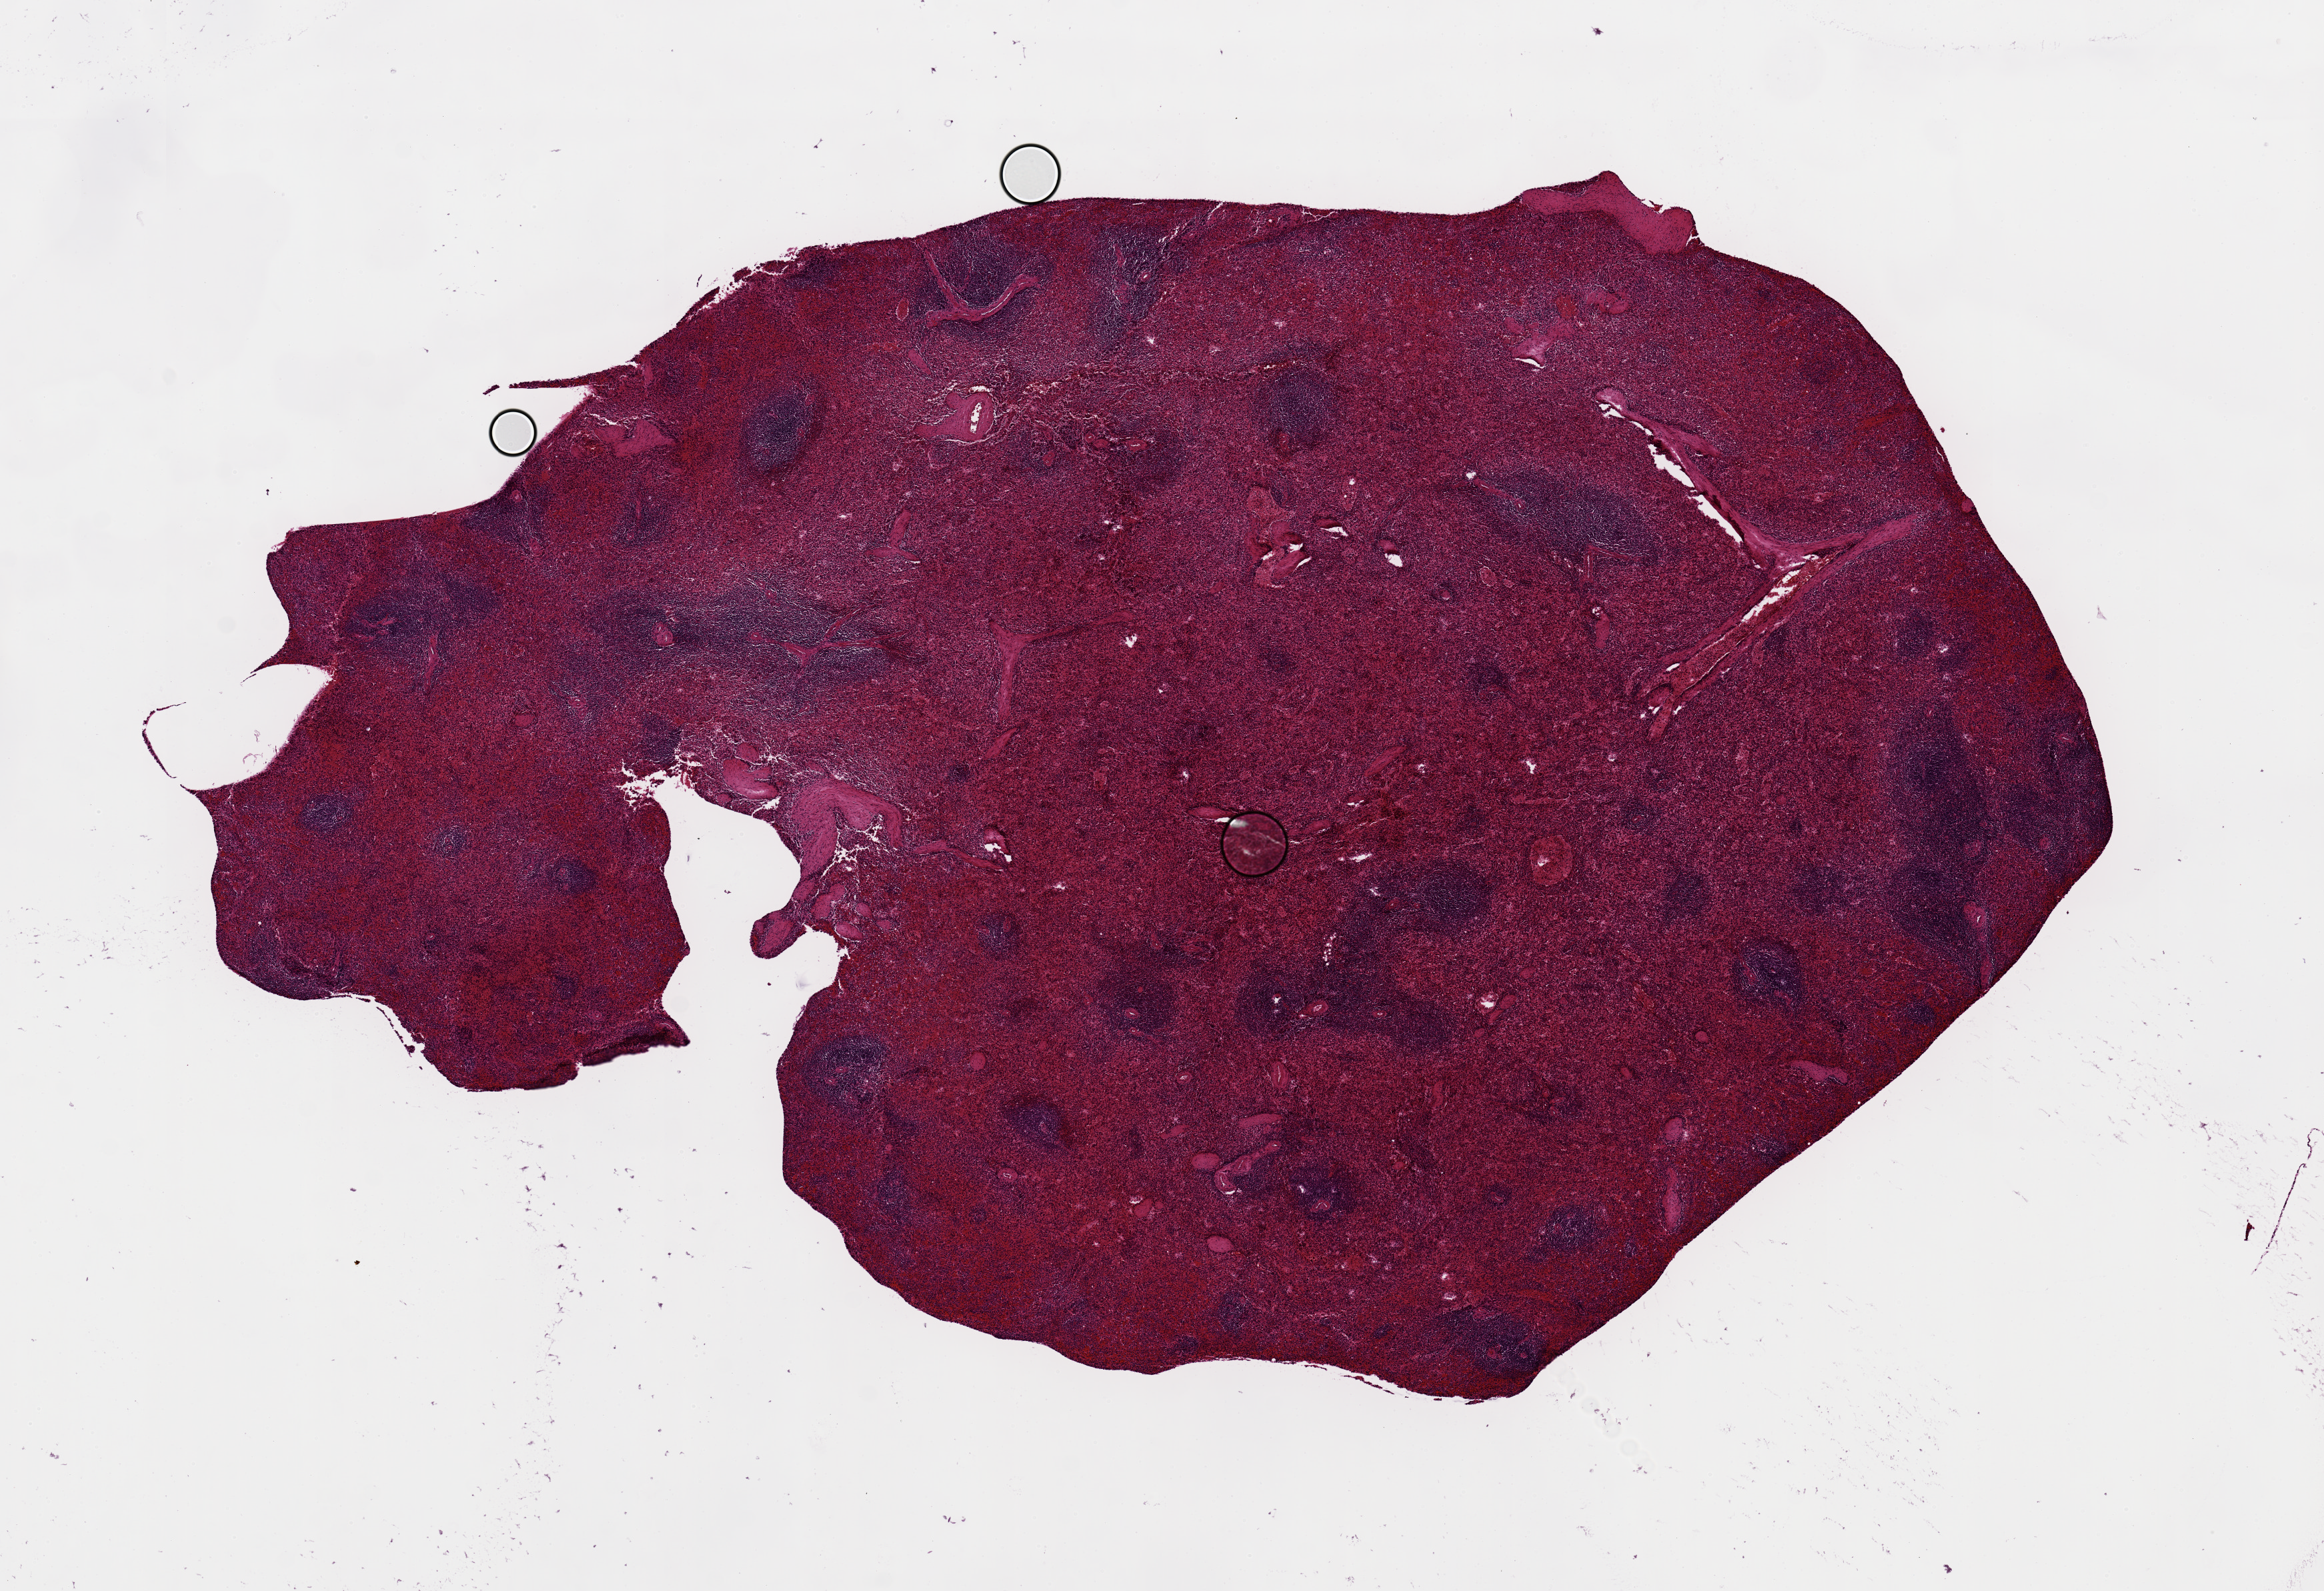
Haematoxylin and eosin whole-slide image — low-resolution overview of the scanned area, about 13.8 x 9.4 mm. PAXgene-fixed paraffin-embedded (PFPE) section. Target tissue: spleen. Donor tissue sample. Donor: male.
Reviewer comment on this tissue sample: Mild congestion. 10x7mm aliquot.